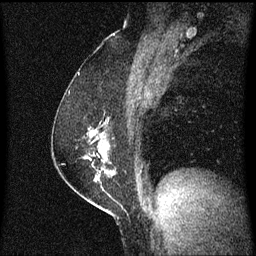
Breast MRI (dynamic contrast-enhanced), one sagittal slice. Position 38 of 60 along the scan axis. Dynamic contrast-enhanced series, image 2 of 3 at this slice position (ordered by acquisition). 1.5 T. TE 4.2 ms, TR 8.4 ms. 2 mm slice thickness. 256 × 256 image matrix, field of view 200 × 200 mm. Female patient, age 52 years. From the clinical record (not read from this slice): setting: breast cancer imaged before/during neoadjuvant chemotherapy; receptor status: HER2-positive.
Structures marked on this image (semi-automatically segmented with operator editing):
- analysis volume of interest (the breast-tissue region the enhancement analysis was run in; not a lesion): bounding box <67,122,108,187> (left, top, right, bottom; pixels)
- tumour enhancement mask (voxels above the 70 % enhancement threshold inside the analysis volume of interest): <91,134,100,177>